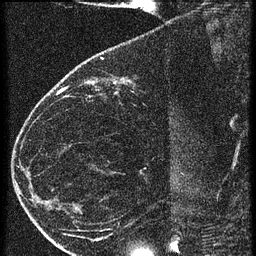
Breast MRI (dynamic contrast-enhanced), one sagittal slice; position 20 of 60 along the scan axis; 3 images stored at this slice position (order not interpretable as contrast timing); 1.5 T; TE 4.2 ms, TR 20.4 ms; 256 × 256 image matrix. Female patient, age 35 years. Case-level facts recorded for this patient, not image findings: setting: breast cancer imaged before/during neoadjuvant chemotherapy; receptor status: HR-positive, HER2-negative.
Outlined on this slice (semi-automatically segmented with operator editing):
- analysis volume of interest (the breast-tissue region the enhancement analysis was run in; not a lesion): bounding box (x1, y1, x2, y2) in pixels: (65, 60, 169, 119)
- tumour enhancement mask (voxels above the 90 % enhancement threshold inside the analysis volume of interest): (121, 78, 124, 83)